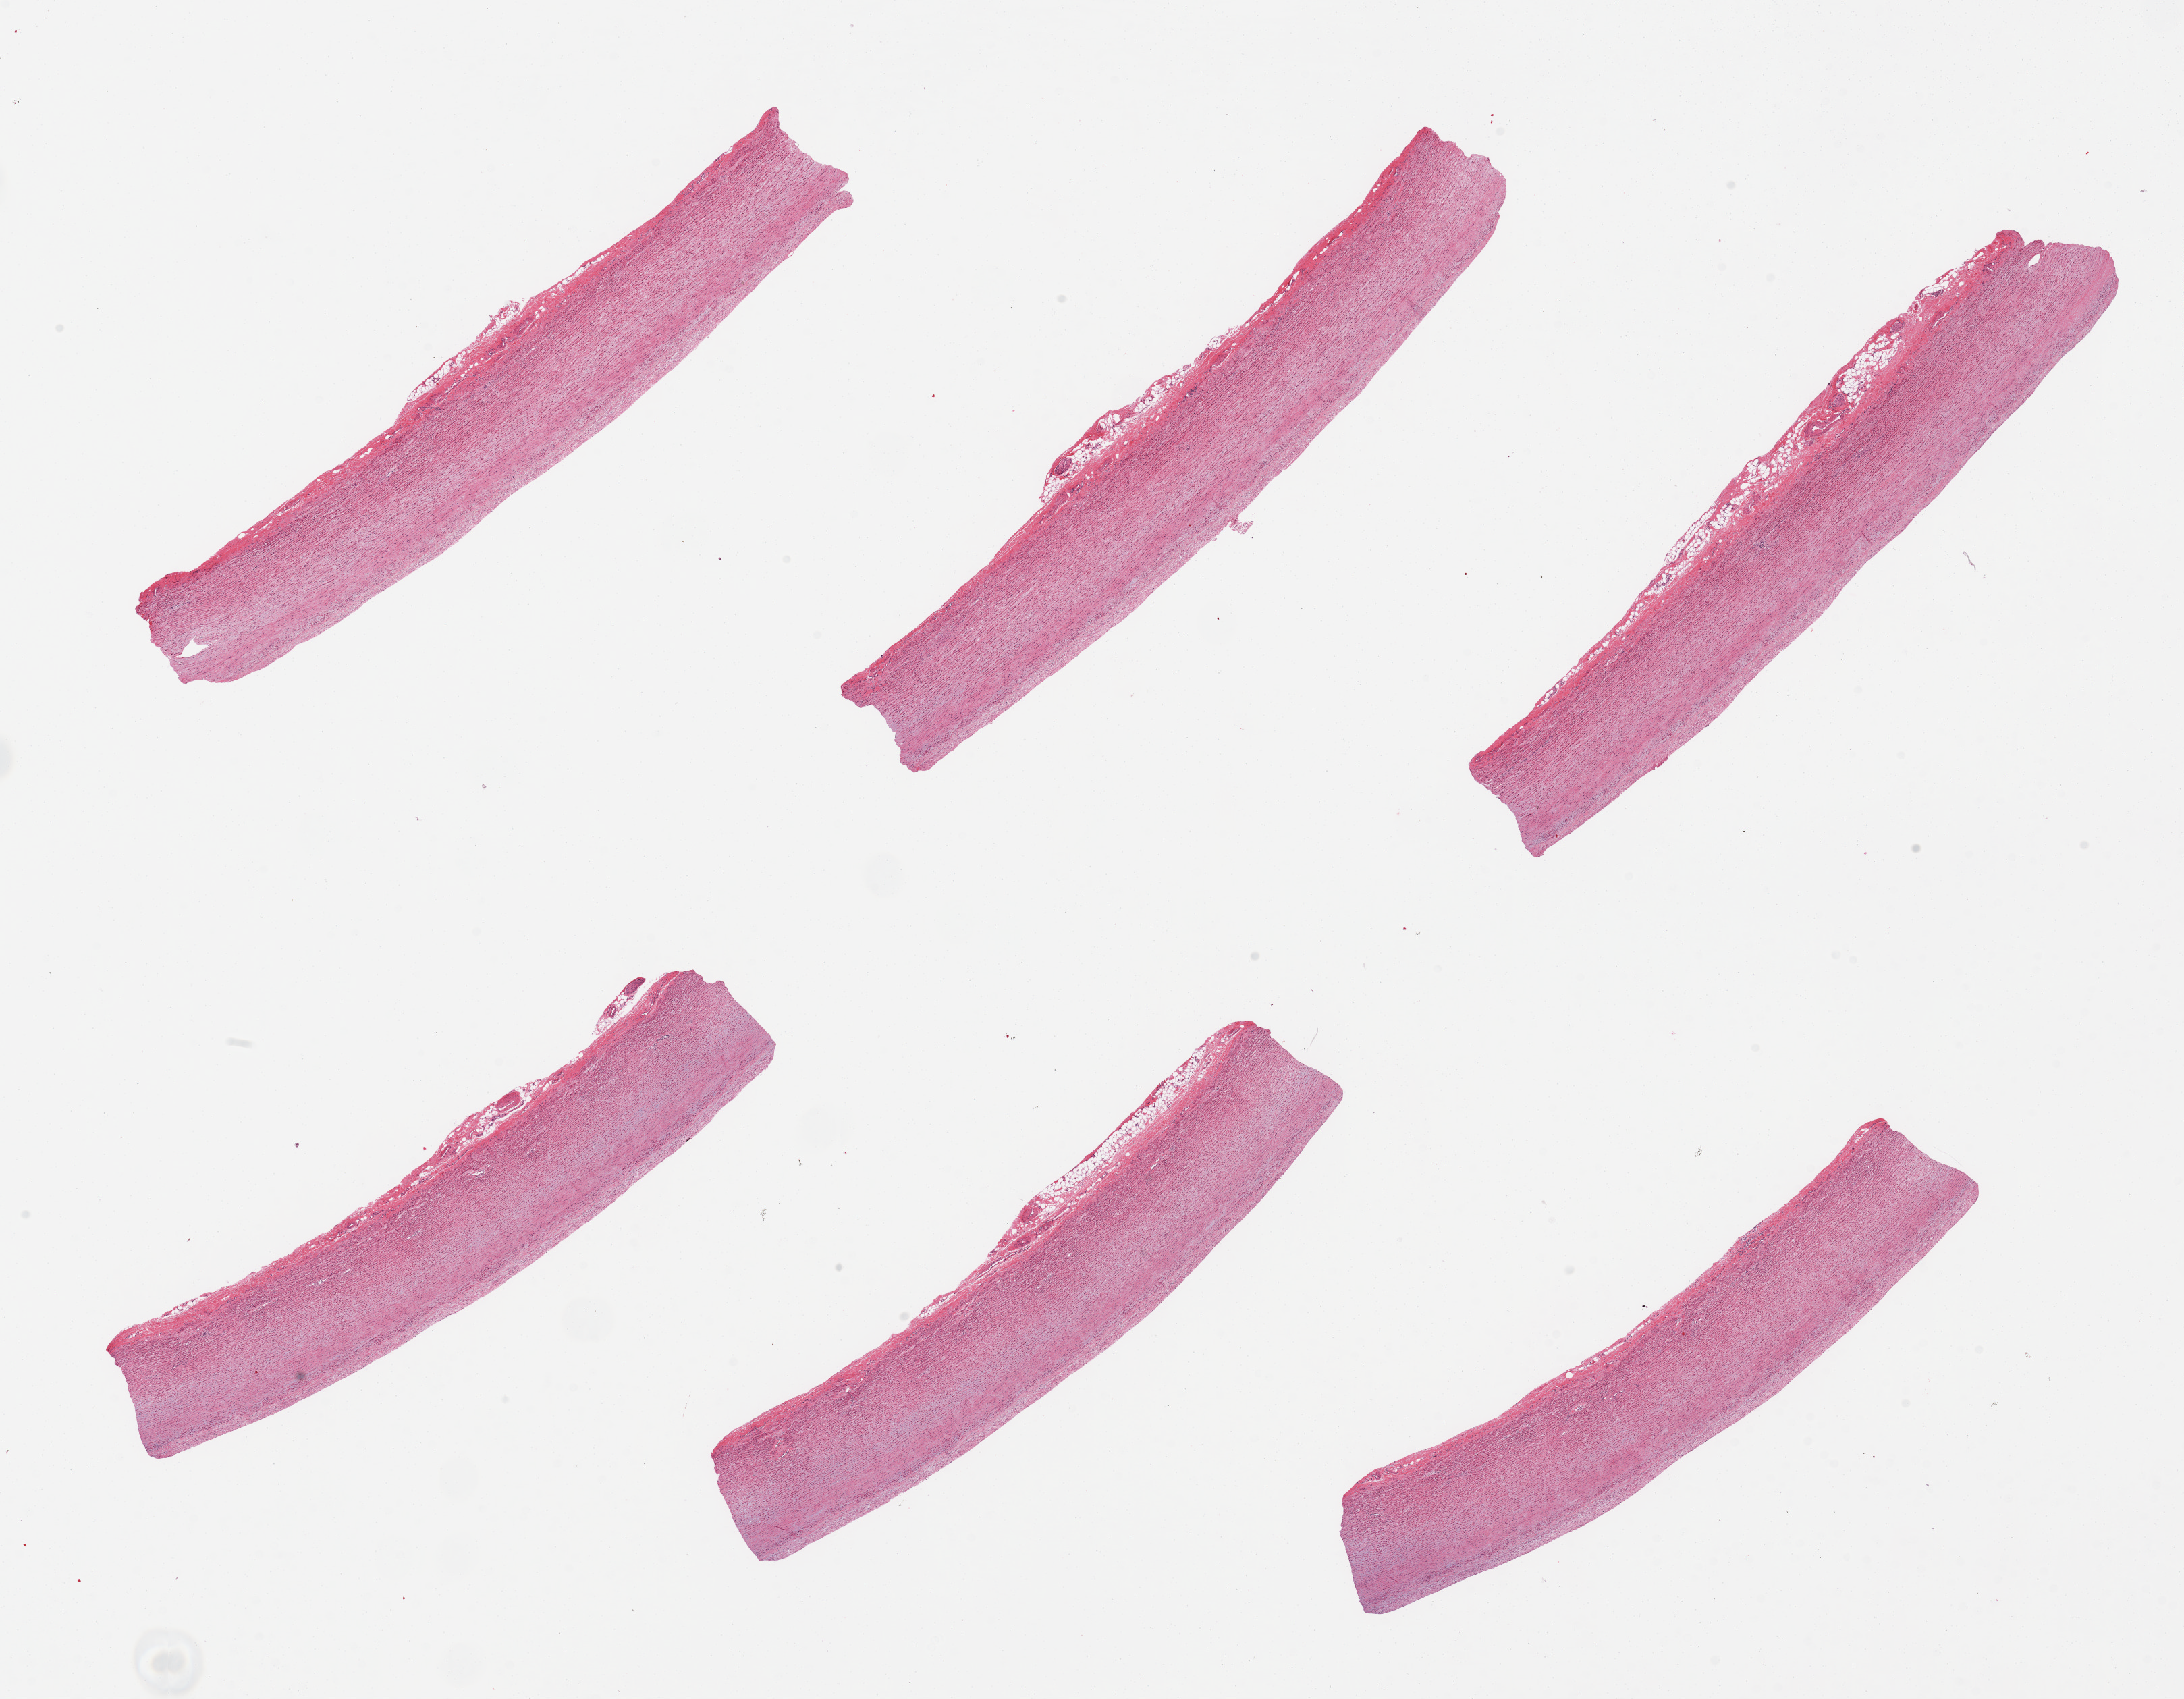
H&E whole-slide image, shown as a low-resolution overview of the whole scanned area (about 25.6 x 19.9 mm); PAXgene-fixed, paraffin-embedded tissue; section of aorta (target tissue); donor tissue sample.
Review note (as recorded): 6 pieces; well trimmed, free of plaques.